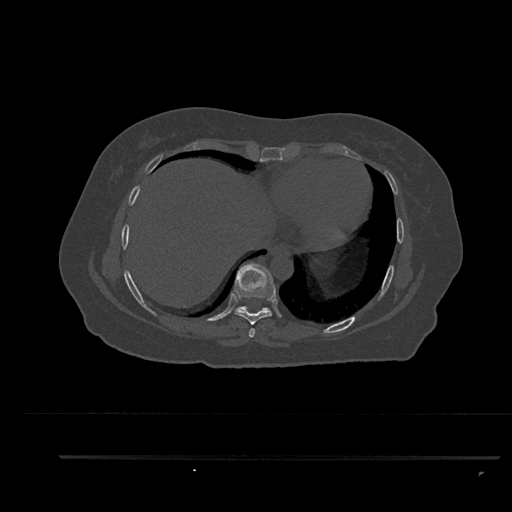
CT including the spine, one axial slice; slice 450 of 797 in the series (ordered by position); reconstruction kernel Br40s/3; bone window (W 1800 / L 400 HU); 512 × 512 image matrix, field of view 408 × 408 mm. Patient: female, 44 years. From the clinical record (not read from this slice): primary cancer: renal.
Structures marked on this image (semi-automatic segmentation, software-assisted and operator-edited):
- T7 vertebra: bounding box [x1, y1, x2, y2] px = [249, 328, 255, 338]
- T8 vertebra: [234, 262, 276, 325]
- T9 vertebra: [235, 306, 269, 313]